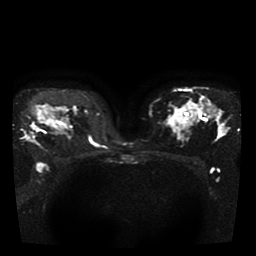
Breast MRI, one axial slice. Position 26 of 41 along the scan axis. Diffusion-weighted series; image 2 of 4 stored at this slice position (different b-values; order by instance number). 1.5 T. 5 mm slice thickness. 256 × 256 image matrix. Female patient.
Structures marked on this image (expert manual segmentation):
- tumour on diffusion-weighted imaging: bounding box [x1, y1, x2, y2] px = [25, 133, 36, 143]